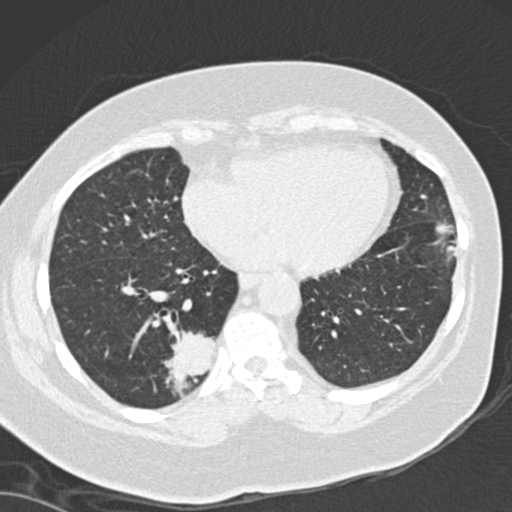
Low-dose screening chest CT, one axial slice. Reconstruction kernel B30f. 120 kVp. Lung window (W 1500 / L -600 HU). 2 mm slice thickness. 512 × 512 image matrix, field of view 328 × 328 mm.
Annotated regions visible in this slice (expert manual segmentation):
- lesion 1 (tumor, lower lobe of right lung): bounding box [x1, y1, x2, y2] px = [164, 330, 216, 395]